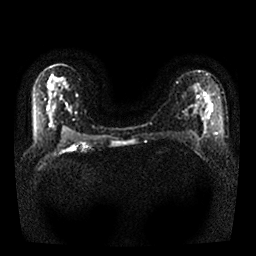
Breast MRI, one axial slice. Position 15 of 25 along the scan axis. Diffusion-weighted series; image 2 of 4 stored at this slice position (different b-values; order by instance number). 1.5 T. 4 mm slice thickness. 256 × 256 image matrix, field of view 340 × 340 mm. Female patient.
Outlined on this slice (outlined manually by an expert reader):
- tumour on diffusion-weighted imaging: bounding box <205,98,212,116> (left, top, right, bottom; pixels)